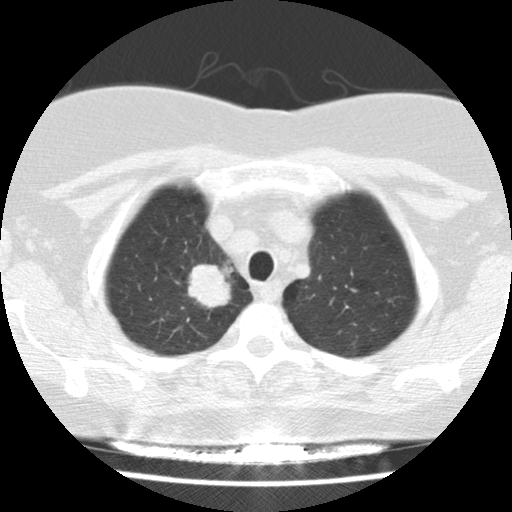
Low-dose screening chest CT, one axial slice. Slice 128 of 148 in the series (ordered by position). Reconstruction kernel STANDARD. Lung window (W 1500 / L -600 HU). 512 × 512 image matrix.
Outlined on this slice (manually delineated by an expert):
- lesion 1 (tumor, upper lobe of right lung): bounding box (x1, y1, x2, y2) in pixels: (188, 264, 231, 308)